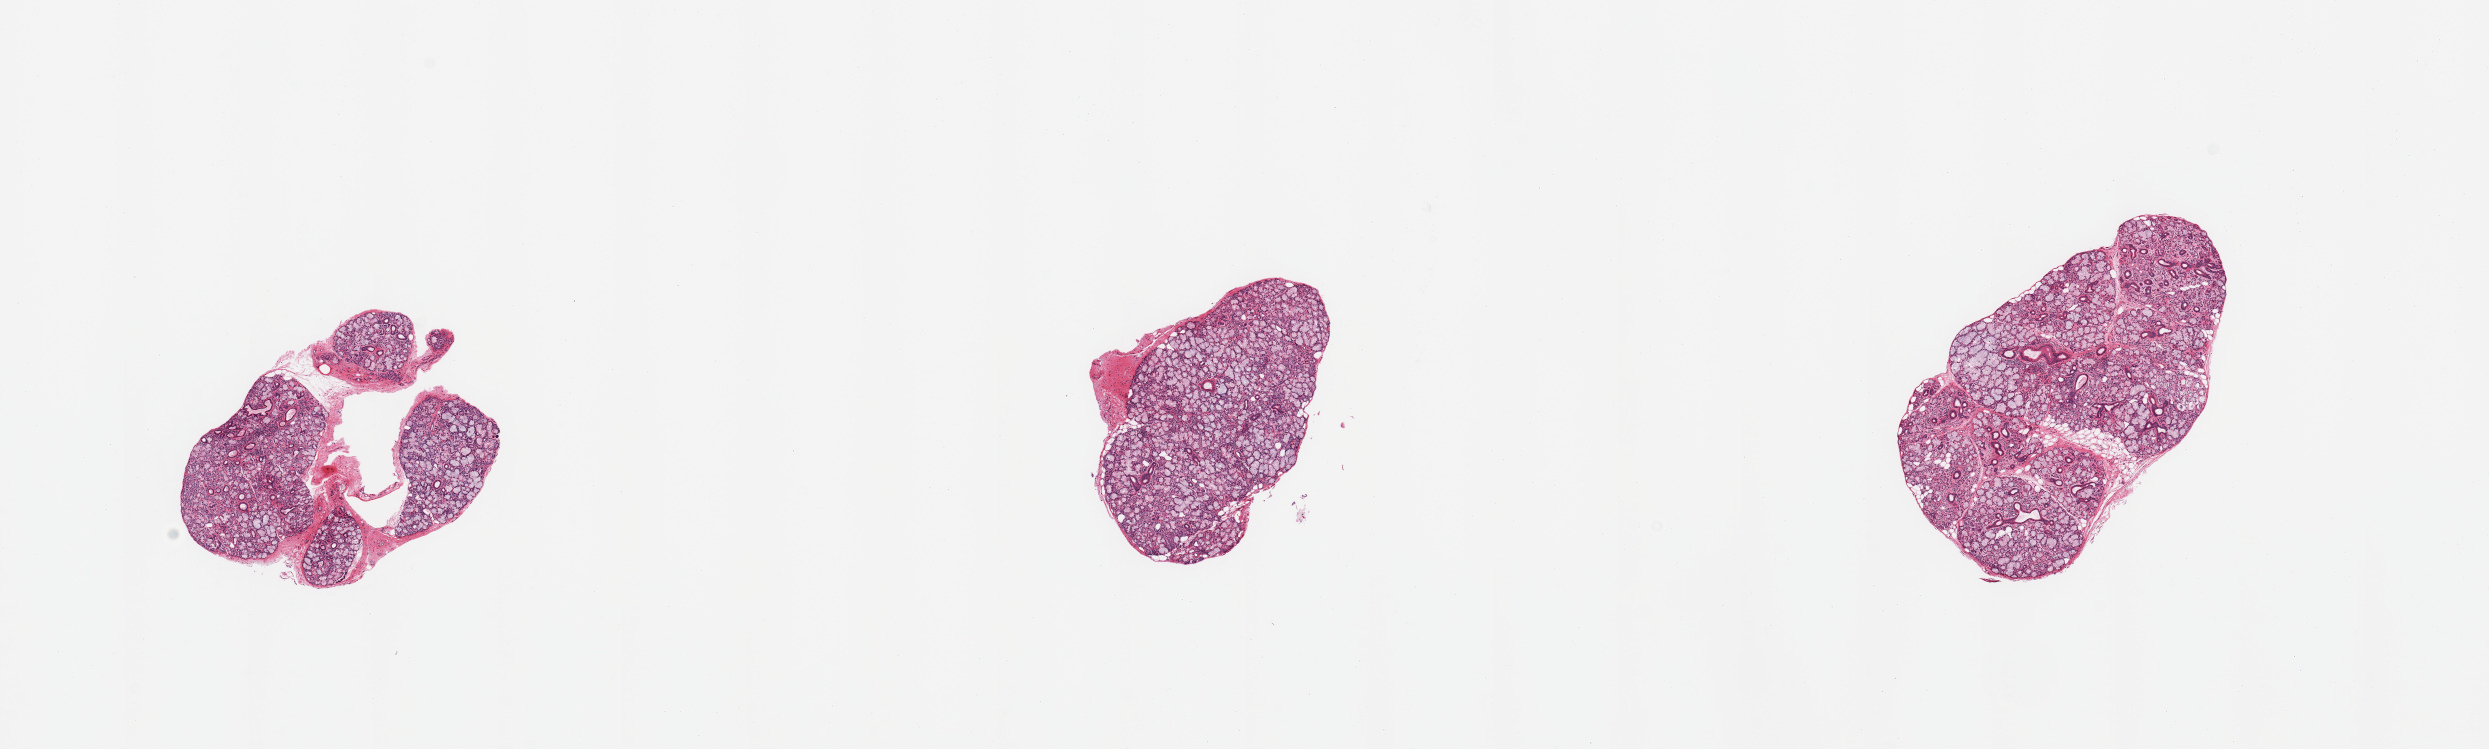
Whole-slide image, haematoxylin and eosin stain, brightfield — a low-resolution overview of the entire scanned area, about 19.7 x 5.9 mm, PAXgene-fixed paraffin-embedded (PFPE) section, section of minor salivary gland (target tissue), tissue donor sample. Donor: female.
Review note (as recorded): 3 pieces, nearly pure glandular elements; excellent specimen.